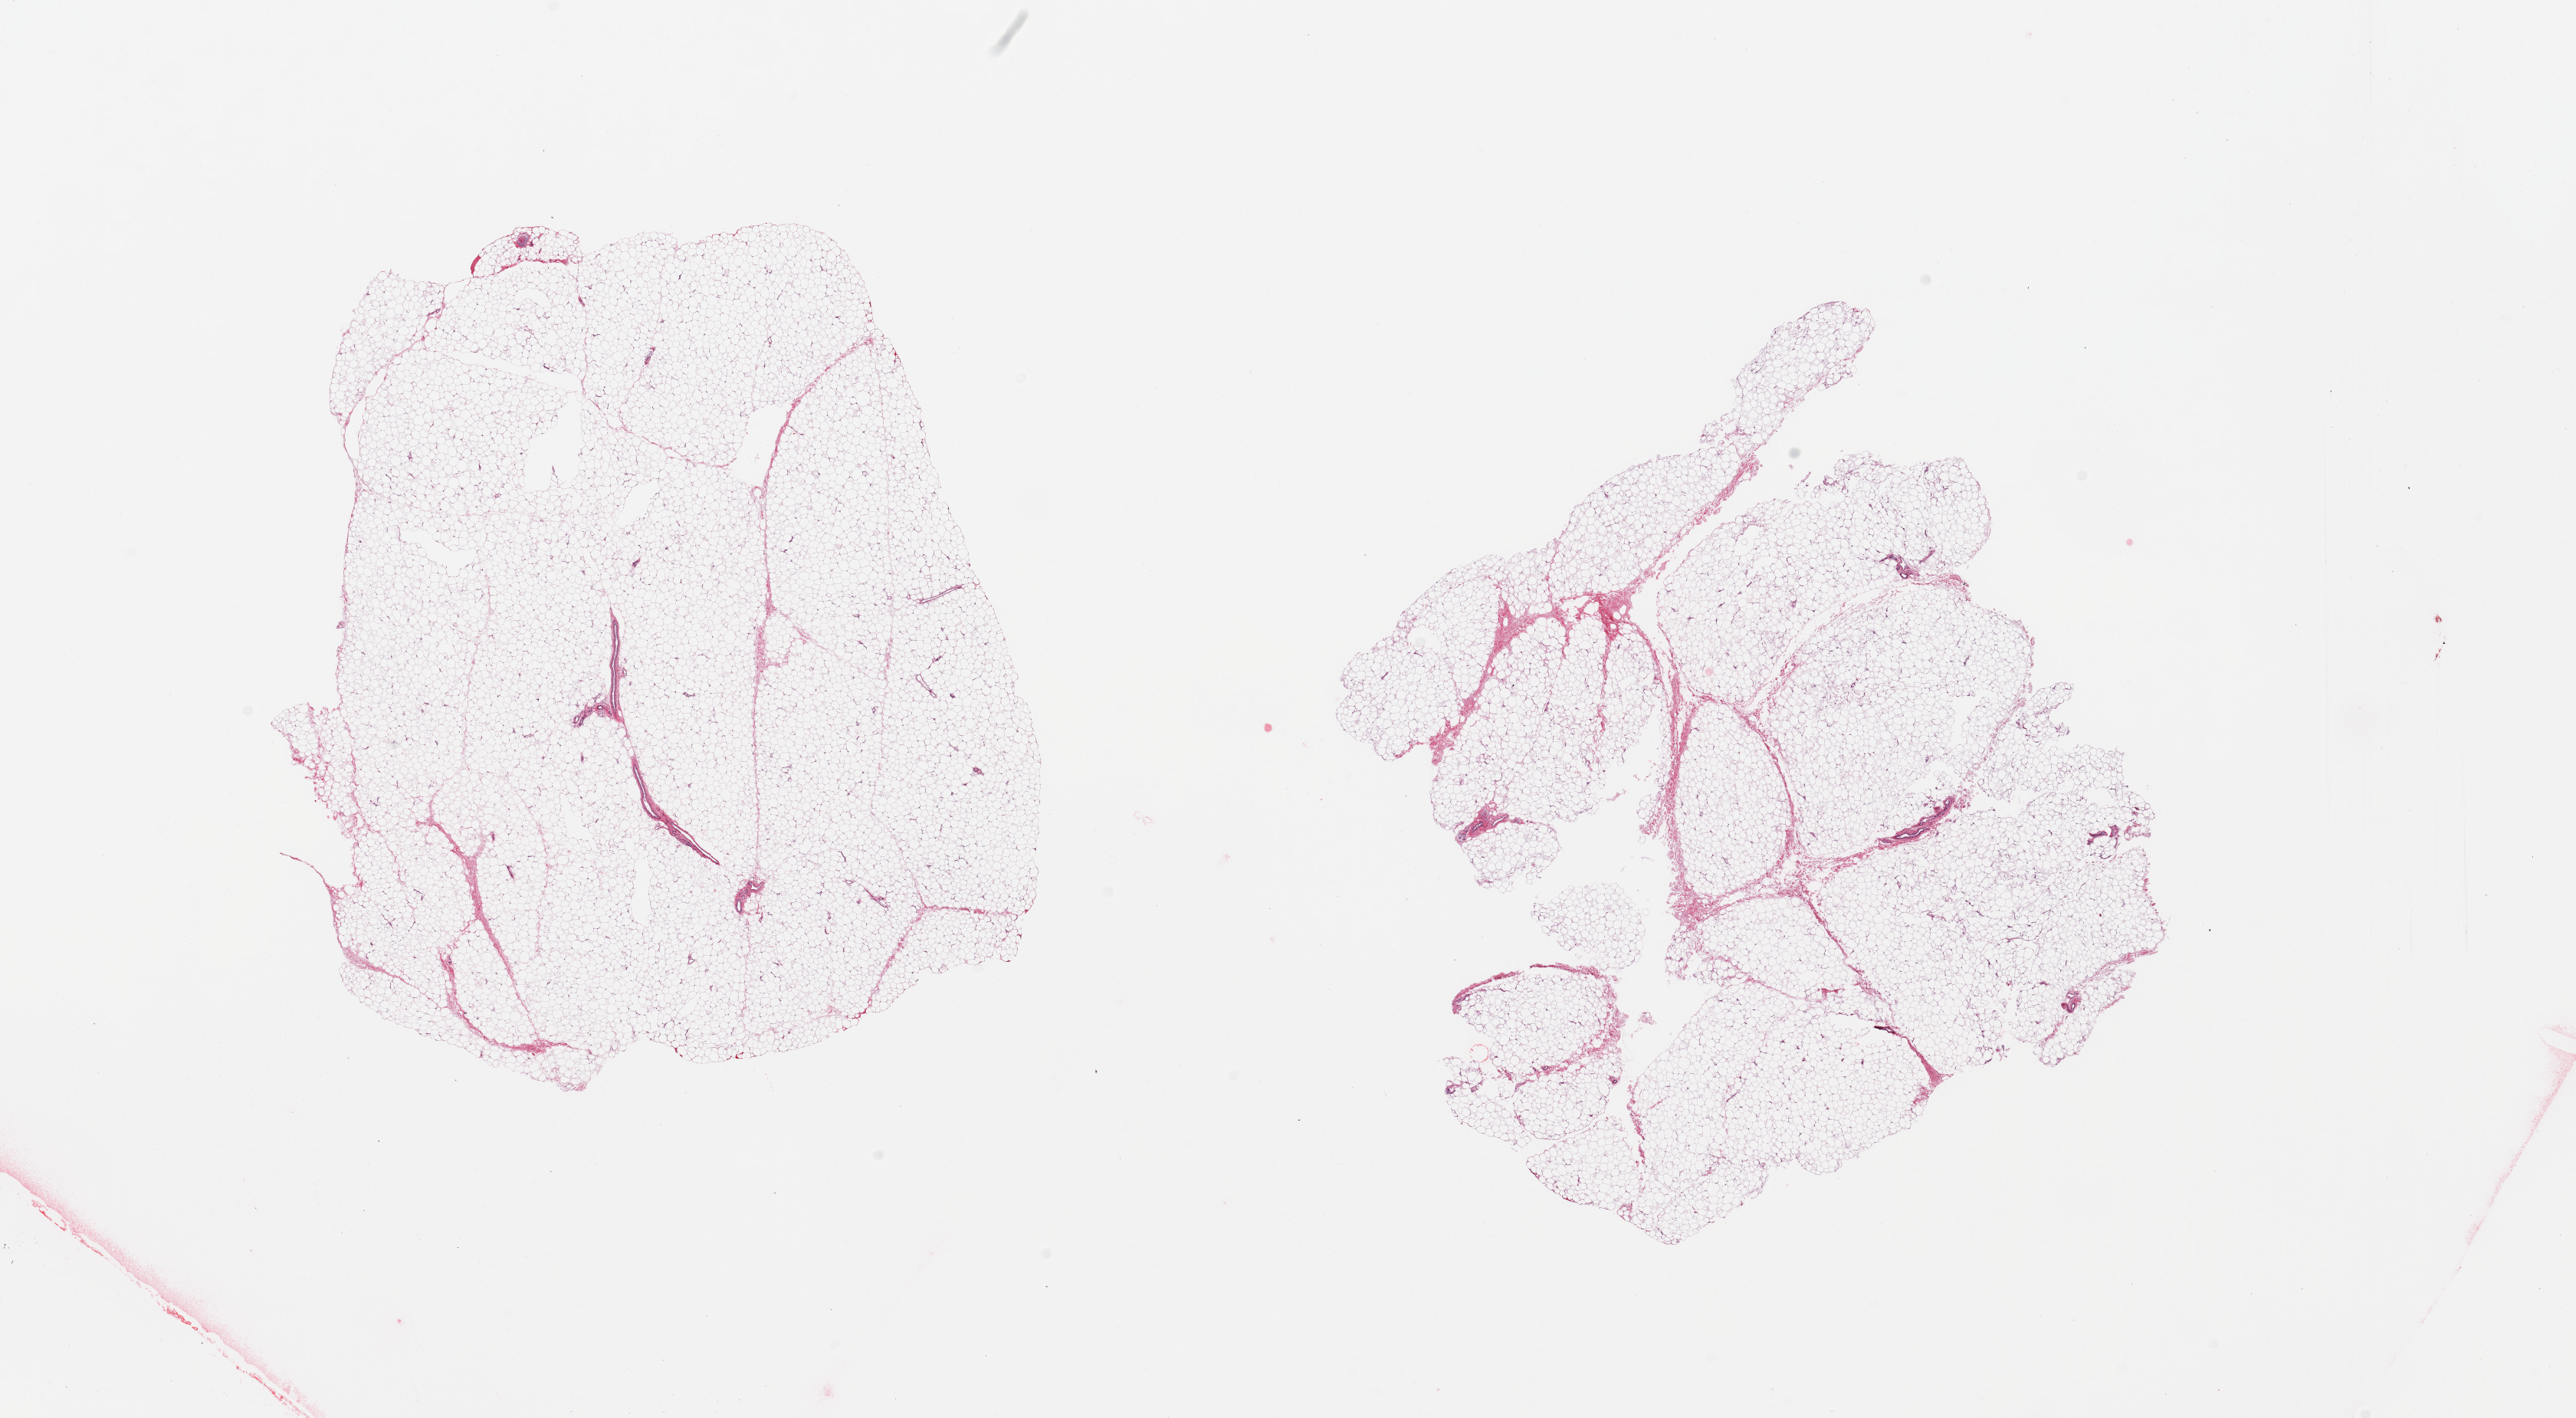
Digitized H&E-stained section, brightfield, shown as a low-resolution overview of the whole scanned area (about 26.6 x 14.6 mm), PAXgene-fixed paraffin-embedded (PFPE) section, section of adipose tissue (target tissue), tissue donor sample. Donor: female.
Reviewer comment on this tissue sample: 2 pieces; mature fat.